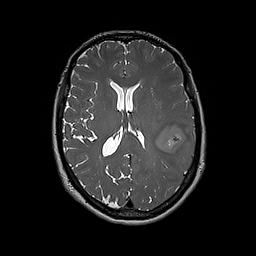
Brain MRI from a brain-tumour surgery series, one axial slice; position 91 of 192 along the scan axis; 1 mm slice thickness; 256 × 256 image matrix, field of view 250 × 250 mm. From the clinical record (not read from this slice): histopathology: Glioblastoma; WHO grade: 4; IDH mutation: no; tumour location: Left Frontal.
Outlined on this slice (manually delineated by an expert):
- tumour: bounding box [x1, y1, x2, y2] px = [155, 118, 195, 167]